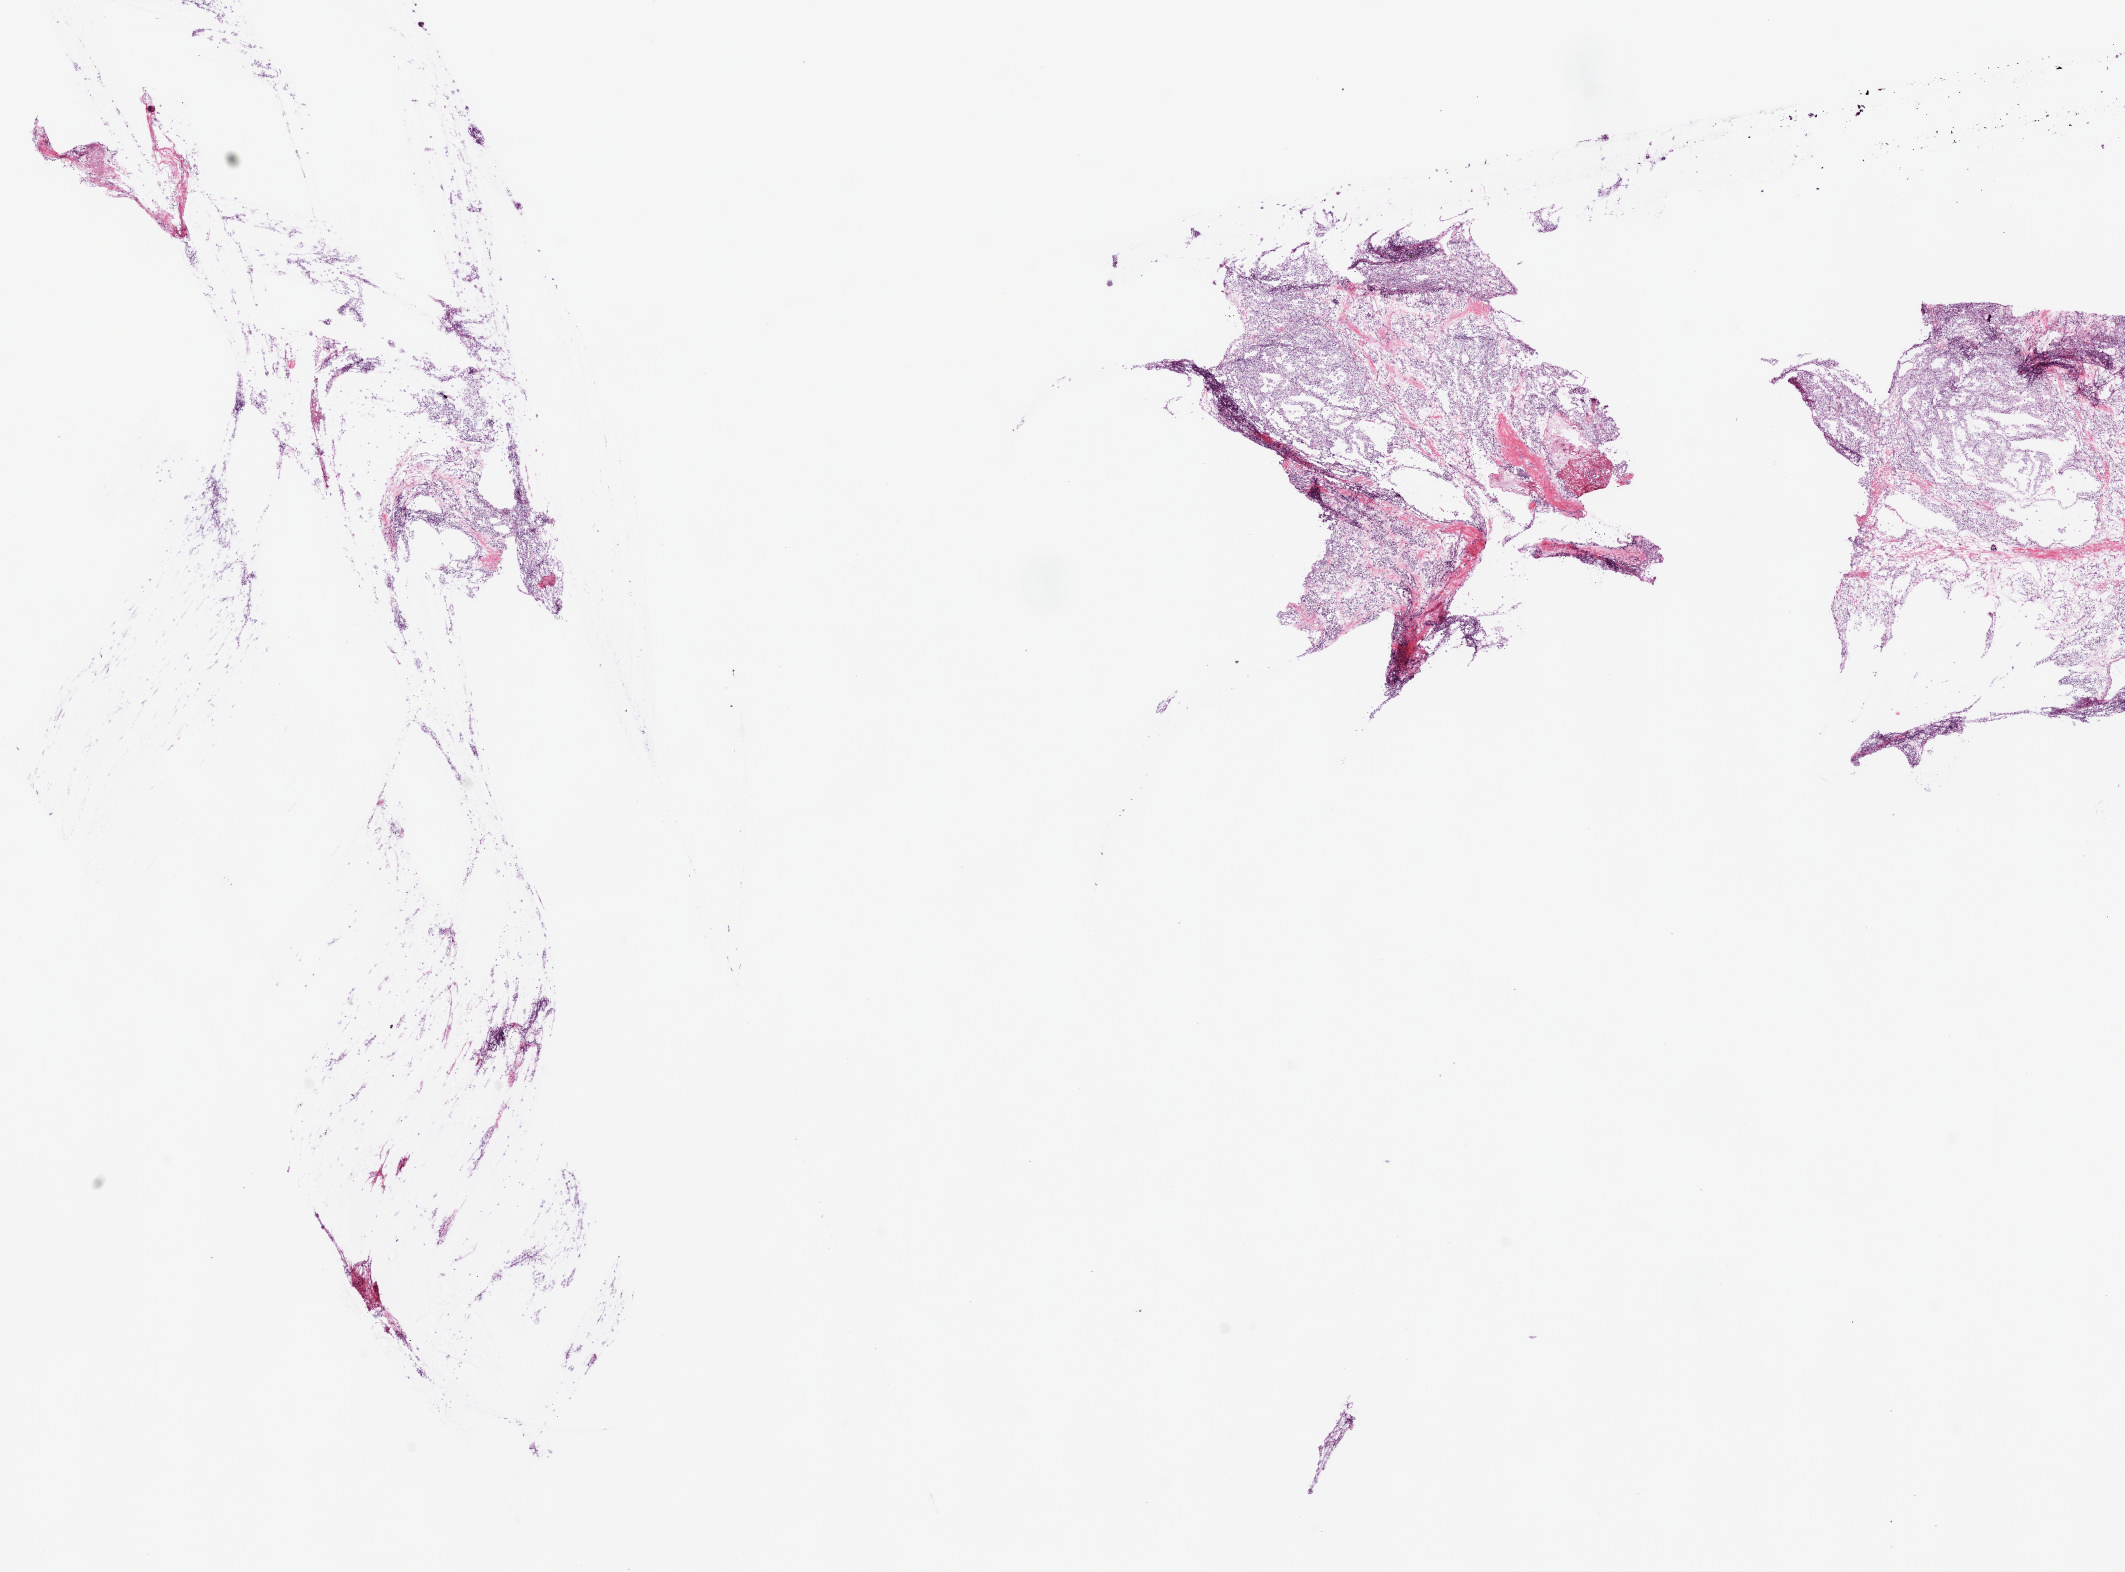
H&E-stained whole-slide image, whole scanned area (about 17.1 x 12.6 mm) shown as a low-resolution overview. Frozen section. Kidney, primary tumour sample. Male, age 35 years at initial diagnosis. Histologic grade: G1 (well differentiated). Slide review estimates, as recorded: tumour cells 92%, tumour nuclei 80%, normal cells 0%, stromal cells 8%, necrosis 0%.
• pathologic diagnosis: Clear cell adenocarcinoma, NOS
• AJCC pathologic stage: I
• laterality: right